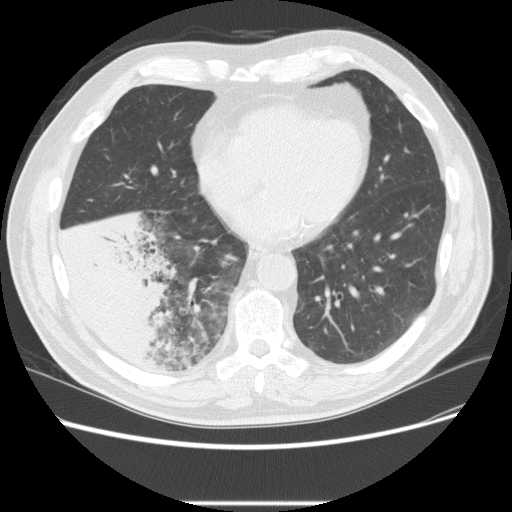
Low-dose screening chest CT, one axial slice. Slice 84 of 233 in the series (ordered by position). Reconstruction kernel STANDARD. 120 kVp. Lung window (W 1500 / L -600 HU). 2.5 mm slice thickness. 512 × 512 image matrix, field of view 380 × 380 mm.
Annotated regions visible in this slice (manually delineated by an expert):
- lesion 3 (tumor, lower lobe of right lung): bounding box <57,209,177,366> (left, top, right, bottom; pixels)